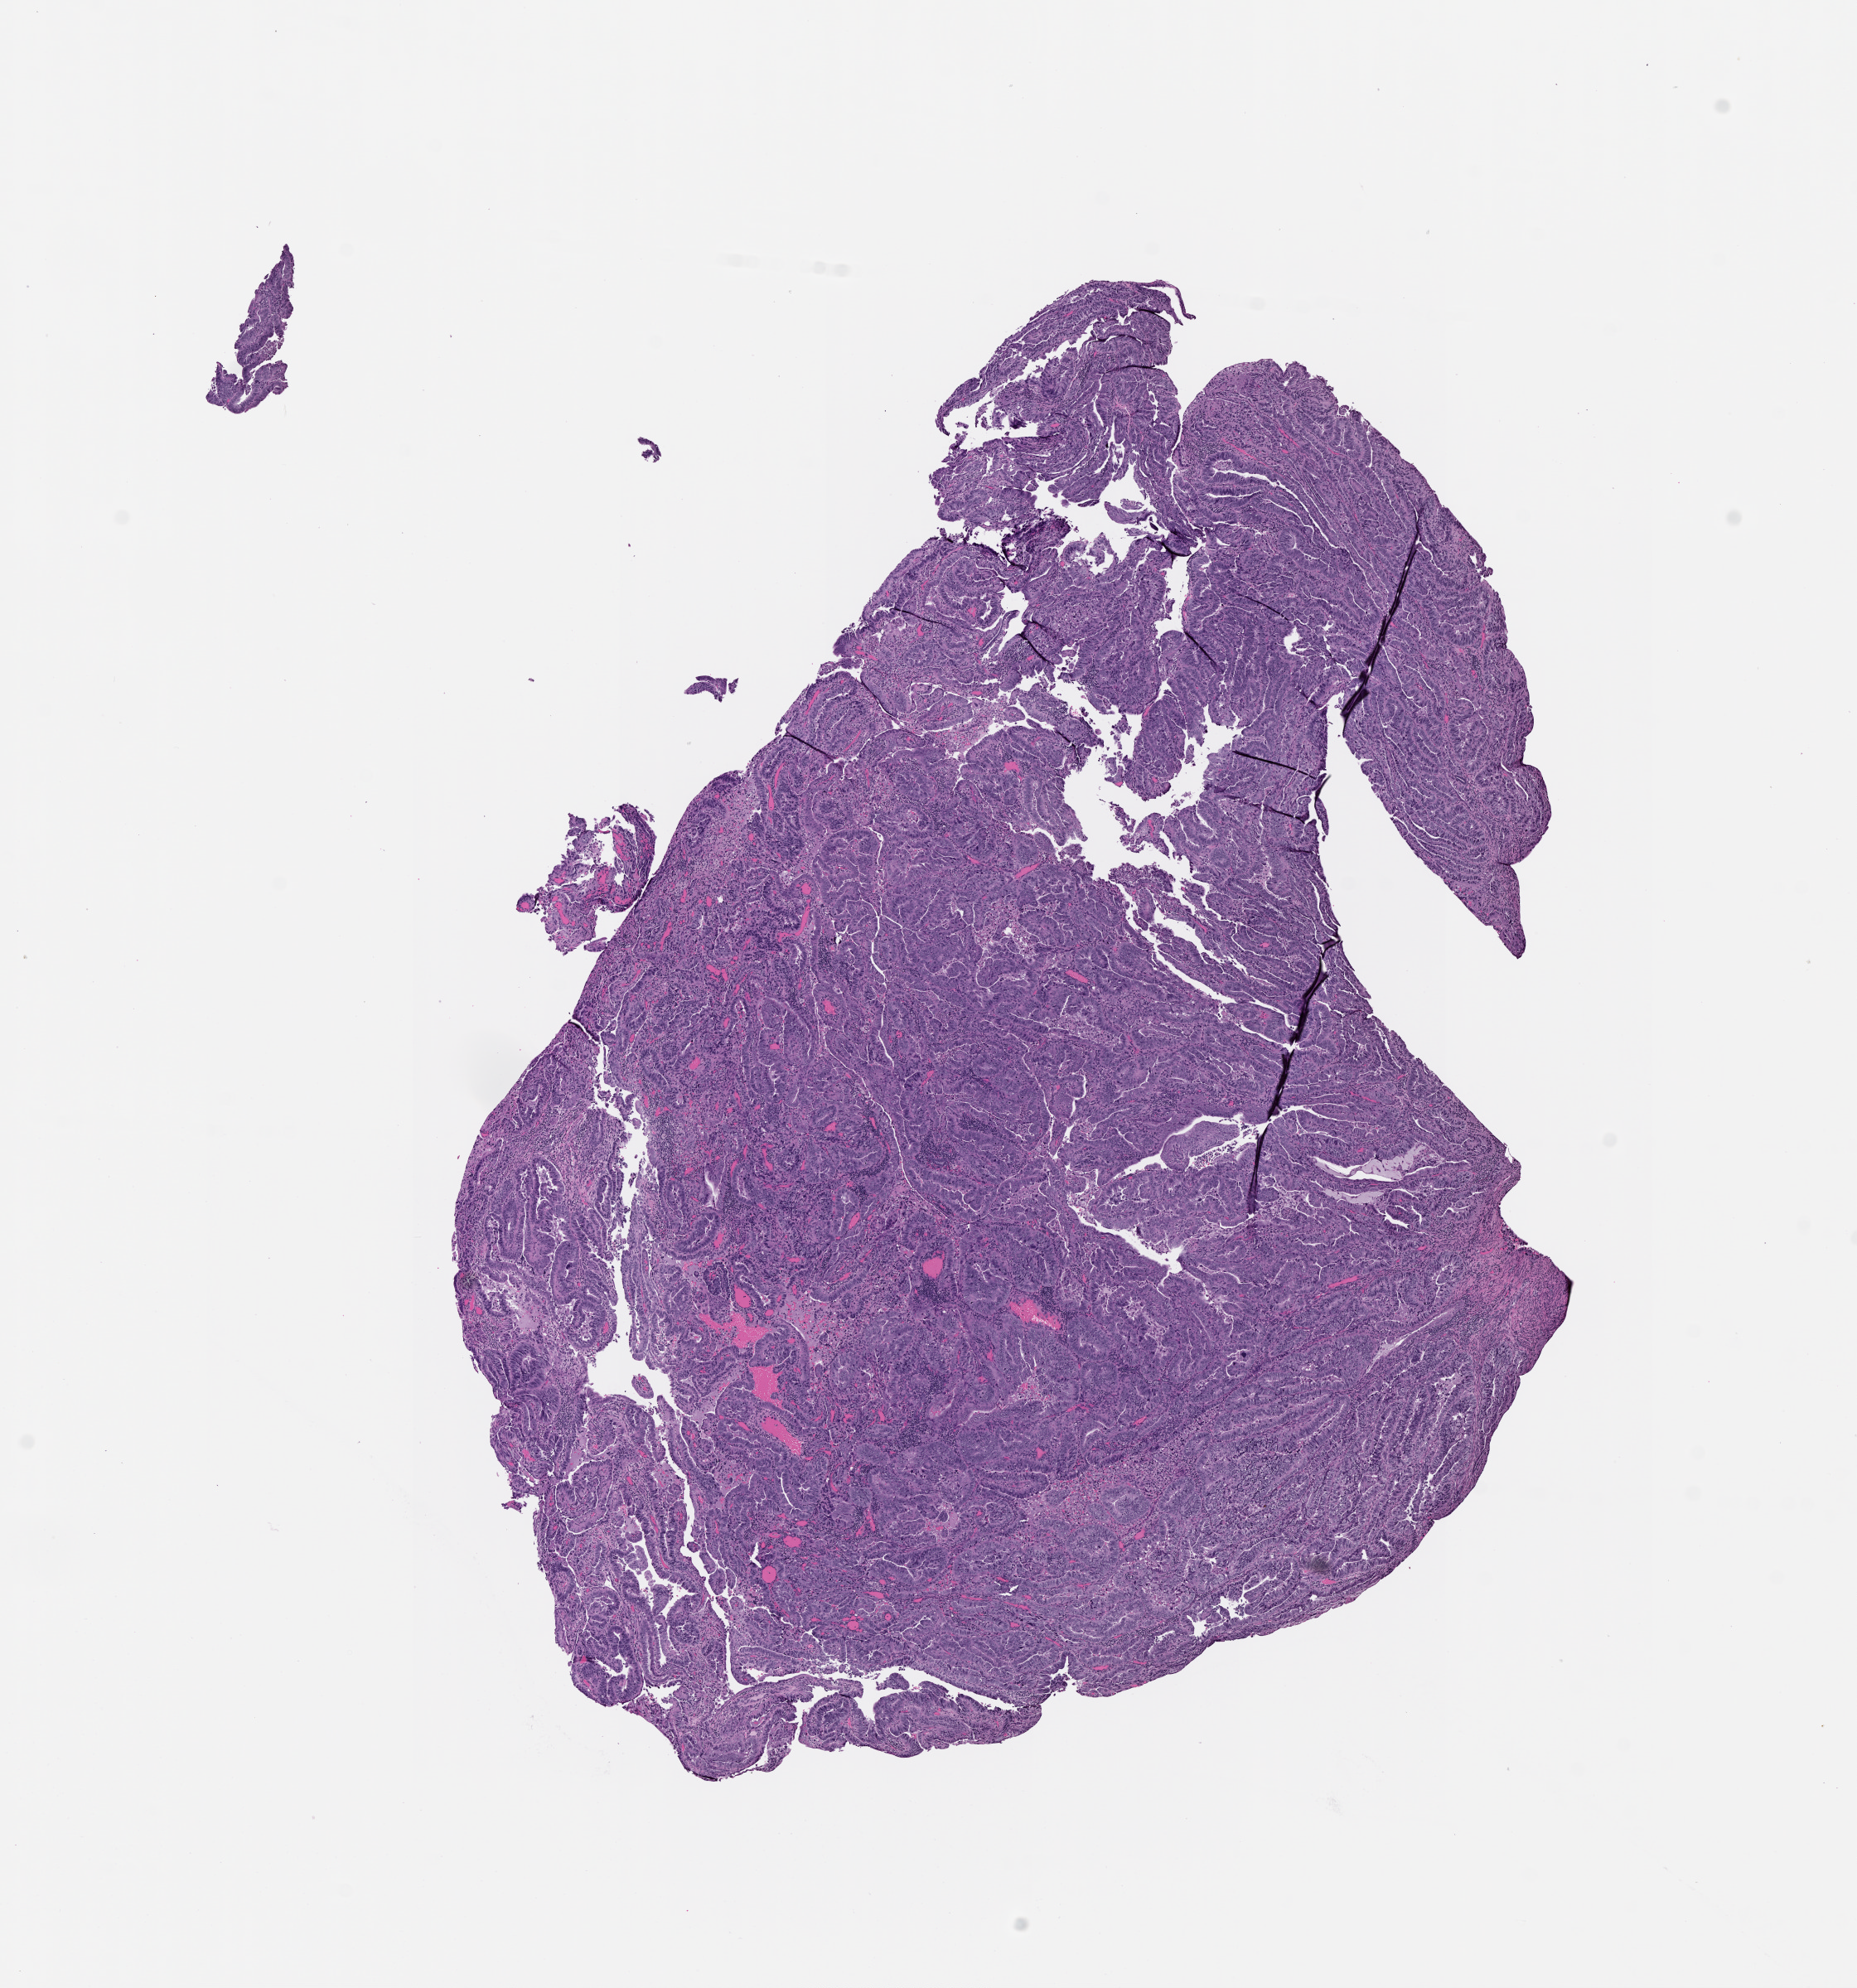
Whole-slide histology image, H&E-stained — whole scanned area (about 9.0 x 9.7 mm, from a 20x scan) shown as a low-resolution overview, tumour tissue sample, uterus. Female, 58 y/o. Histologic grade: G3 (poorly differentiated).
• AJCC pathologic stage: IIIC1
• histologic diagnosis: Endometrioid adenocarcinoma, NOS
• primary tumour site (as recorded): posterior endometrium